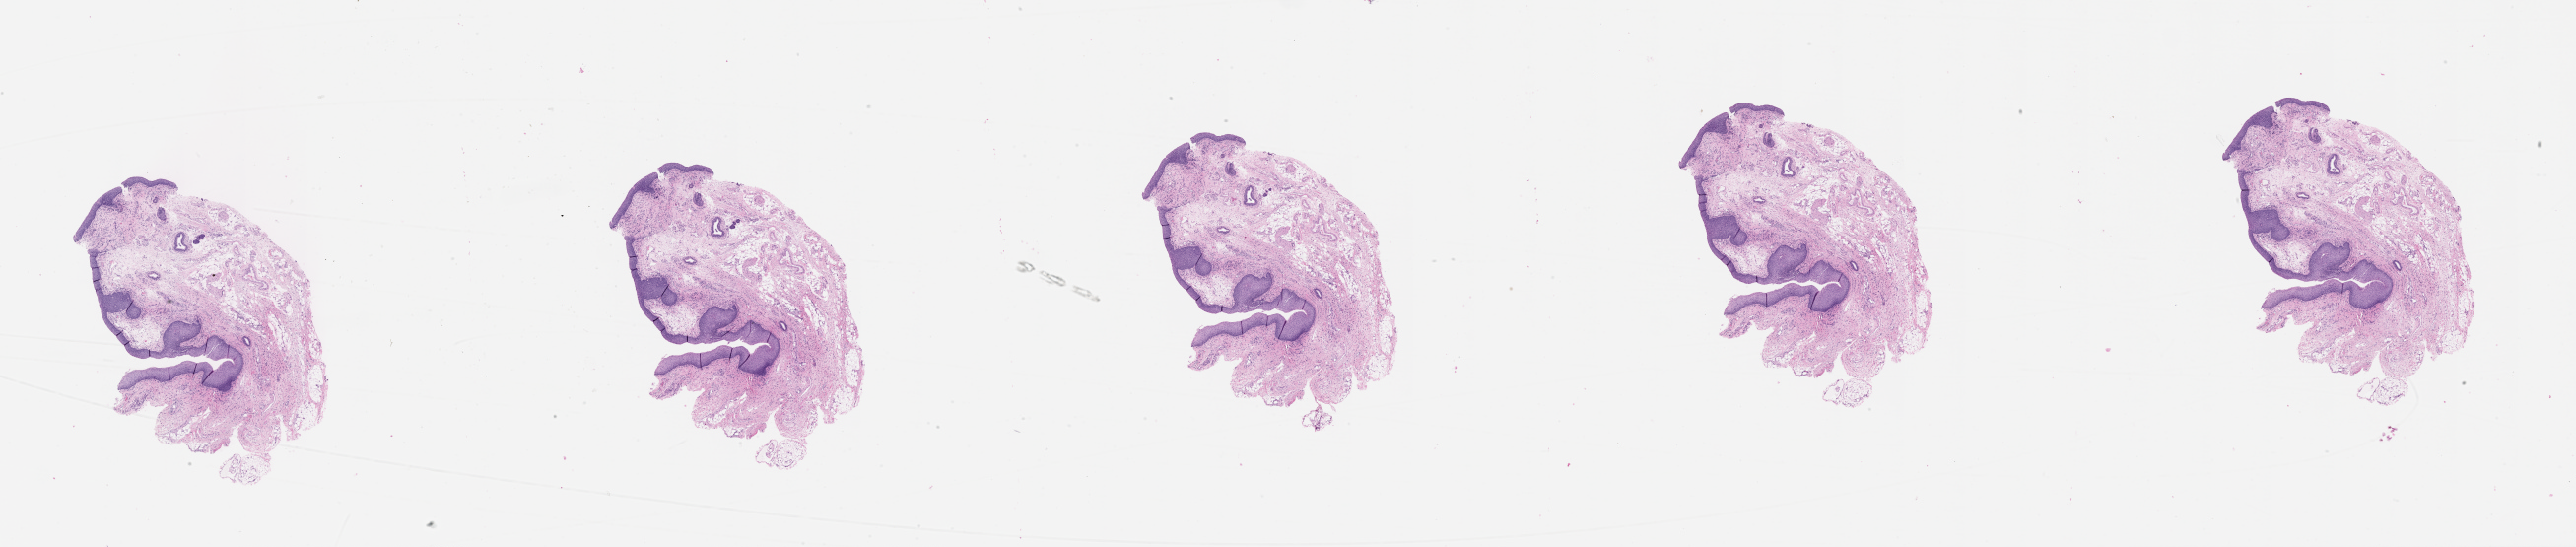
Whole-slide histology image, Hematoxylin and eosin (H&E) stained — whole scanned area (about 42.1 x 8.9 mm, from a 20x scan) shown as a low-resolution overview; head and neck, normal (non-tumour) tissue. 61-year-old female patient.
* this section: normal (non-tumour) tissue from the same patient
* patient diagnosis: Squamous cell carcinoma, NOS (tonsil, NOS)